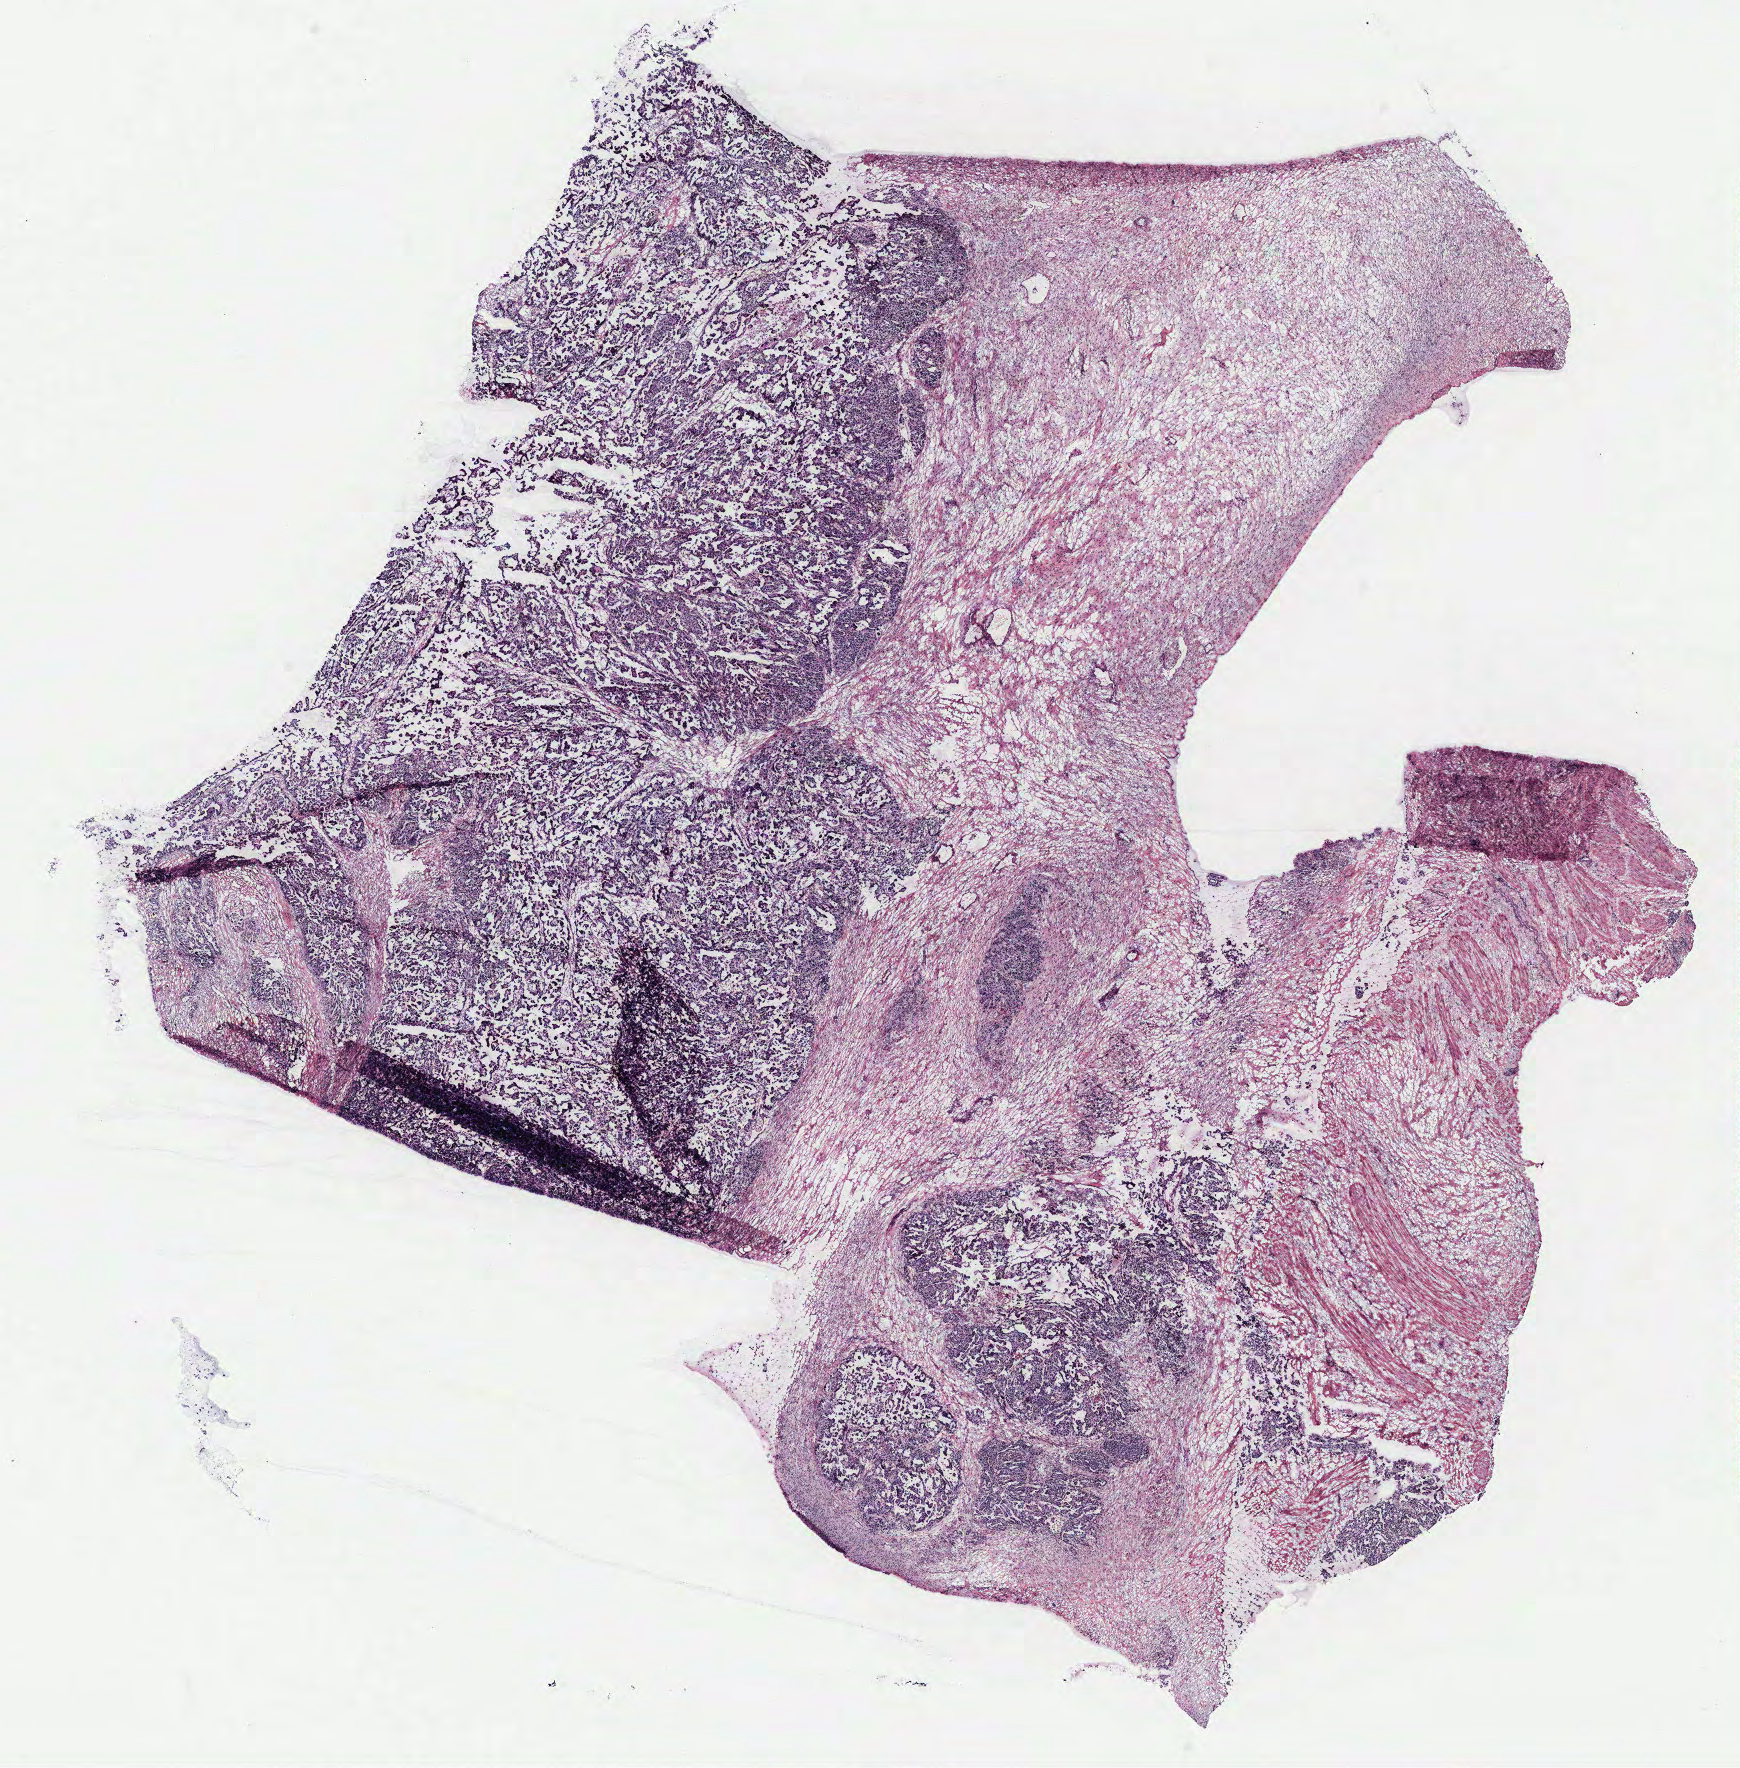
Whole-slide histology image, H&E, shown as a low-resolution overview of the whole scanned area (about 13.9 x 14.1 mm); tumour tissue sample, ovary. Female, 56 y/o.
Primary tumour site (as recorded): ovary. Diagnosis: Serous adenocarcinoma, NOS.